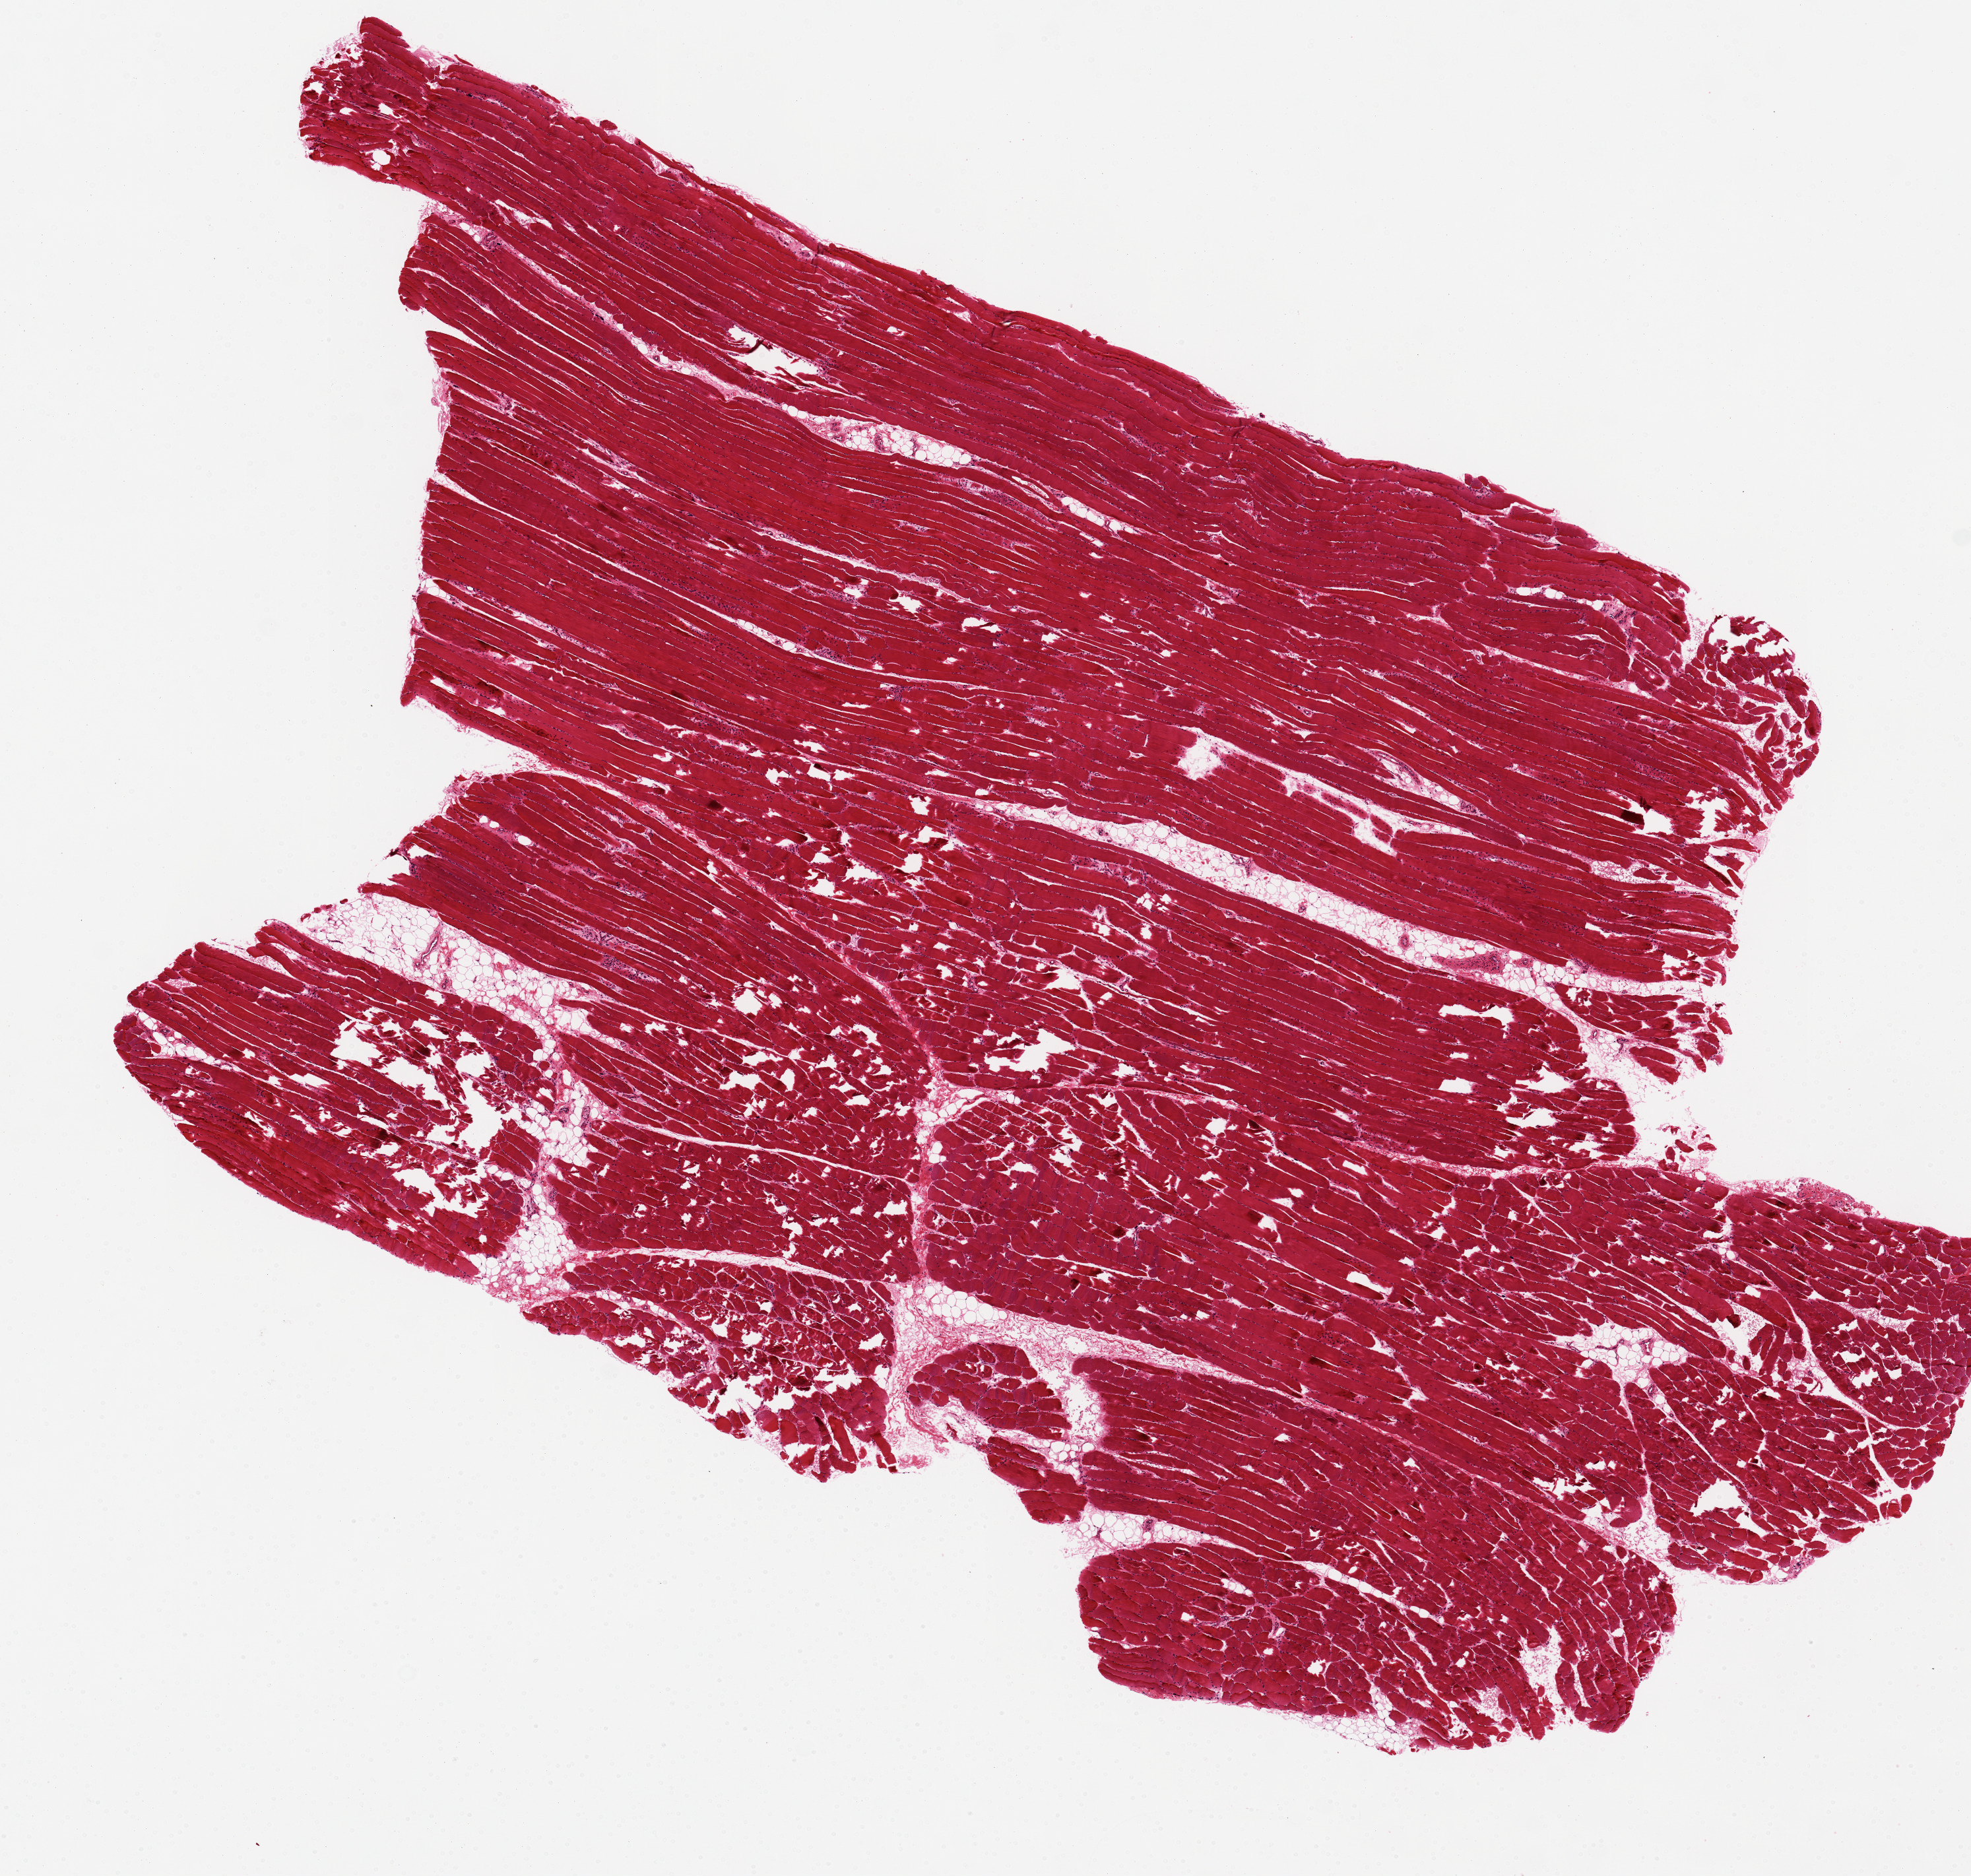
Whole-slide image, hematoxylin and eosin (H&E) stain, brightfield — low-resolution overview of the scanned area, about 11.8 x 11.2 mm (acquisition: 20x scan); PAXgene-fixed, paraffin-embedded tissue; target tissue: skeletal muscle; donor tissue sample. Female donor.
Pathologist's review note for this sample: Numerous defects. 10x6.5mm.